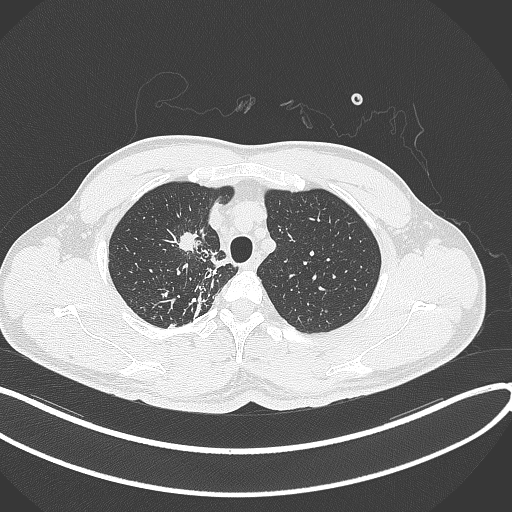
Chest CT, one axial slice. Reconstruction kernel B70f. 120 kVp. Lung window (W 1500 / L -600 HU). 1 mm slice thickness. 512 × 512 image matrix, field of view 400 × 400 mm. Patient: male, 48 years. From the clinical record (not read from this slice): clinical TNM (as recorded): T1c N1 M1.
Annotated regions visible in this slice (bounding box drawn by a radiologist):
- lung tumour (recorded histology: adenocarcinoma): bounding box <176,225,203,256> (left, top, right, bottom; pixels)